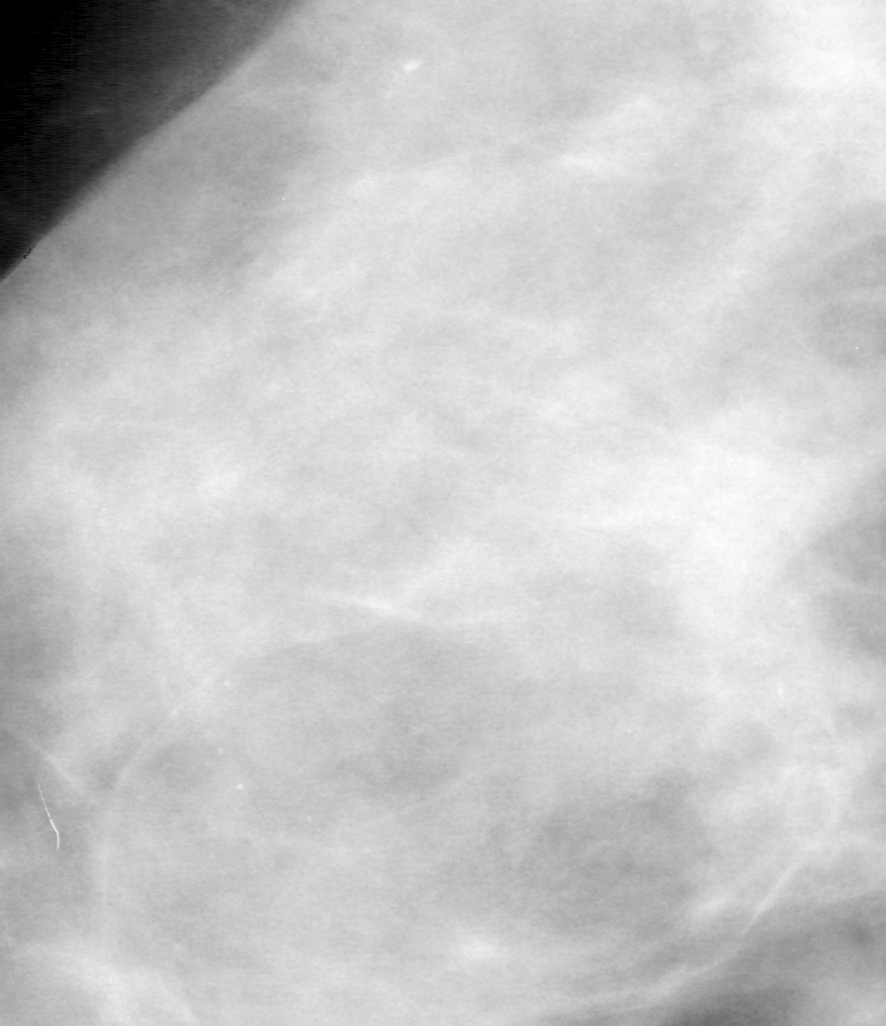
Crop from a digitized film mammogram around one marked abnormality, left breast, CC view, BI-RADS breast density category 4 (scale 1–4).
Finding: calcifications, morphology punctate, distribution regional; BI-RADS assessment category 4; pathology (as recorded): malignant.